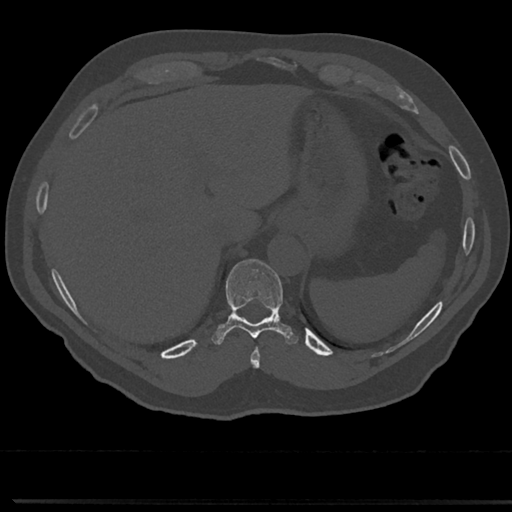
CT including the spine, one axial slice; position 257 of 817 along the scan axis; reconstruction kernel Br40s/3; 120 kVp; bone window (W 1800 / L 400 HU); 0.5 mm slice thickness; 512 × 512 image matrix, field of view 355 × 355 mm. Patient: male, 61 years. From the clinical record (not read from this slice): primary cancer: prostate.
Outlined on this slice (semi-automatically segmented with operator editing):
- T10 vertebra: bounding box [x1, y1, x2, y2] px = [210, 260, 299, 346]
- T9 vertebra: [252, 336, 260, 368]